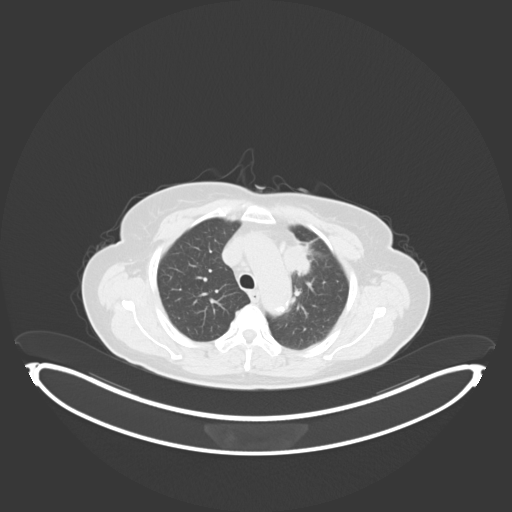
Chest CT, one axial slice. Slice 195 of 243 in the series (ordered by position). Reconstruction kernel B30f. Lung window (W 1500 / L -600 HU). 512 × 512 image matrix, field of view 500 × 500 mm. Patient: female, 65 years. From the clinical record (not read from this slice): clinical TNM (as recorded): T2a N0 M0; histopathological grade: G2-3.
Structures marked on this image (bounding box drawn by a radiologist):
- lung tumour (recorded histology: adenocarcinoma): box from (x=284, y=238) to (x=312, y=277) px